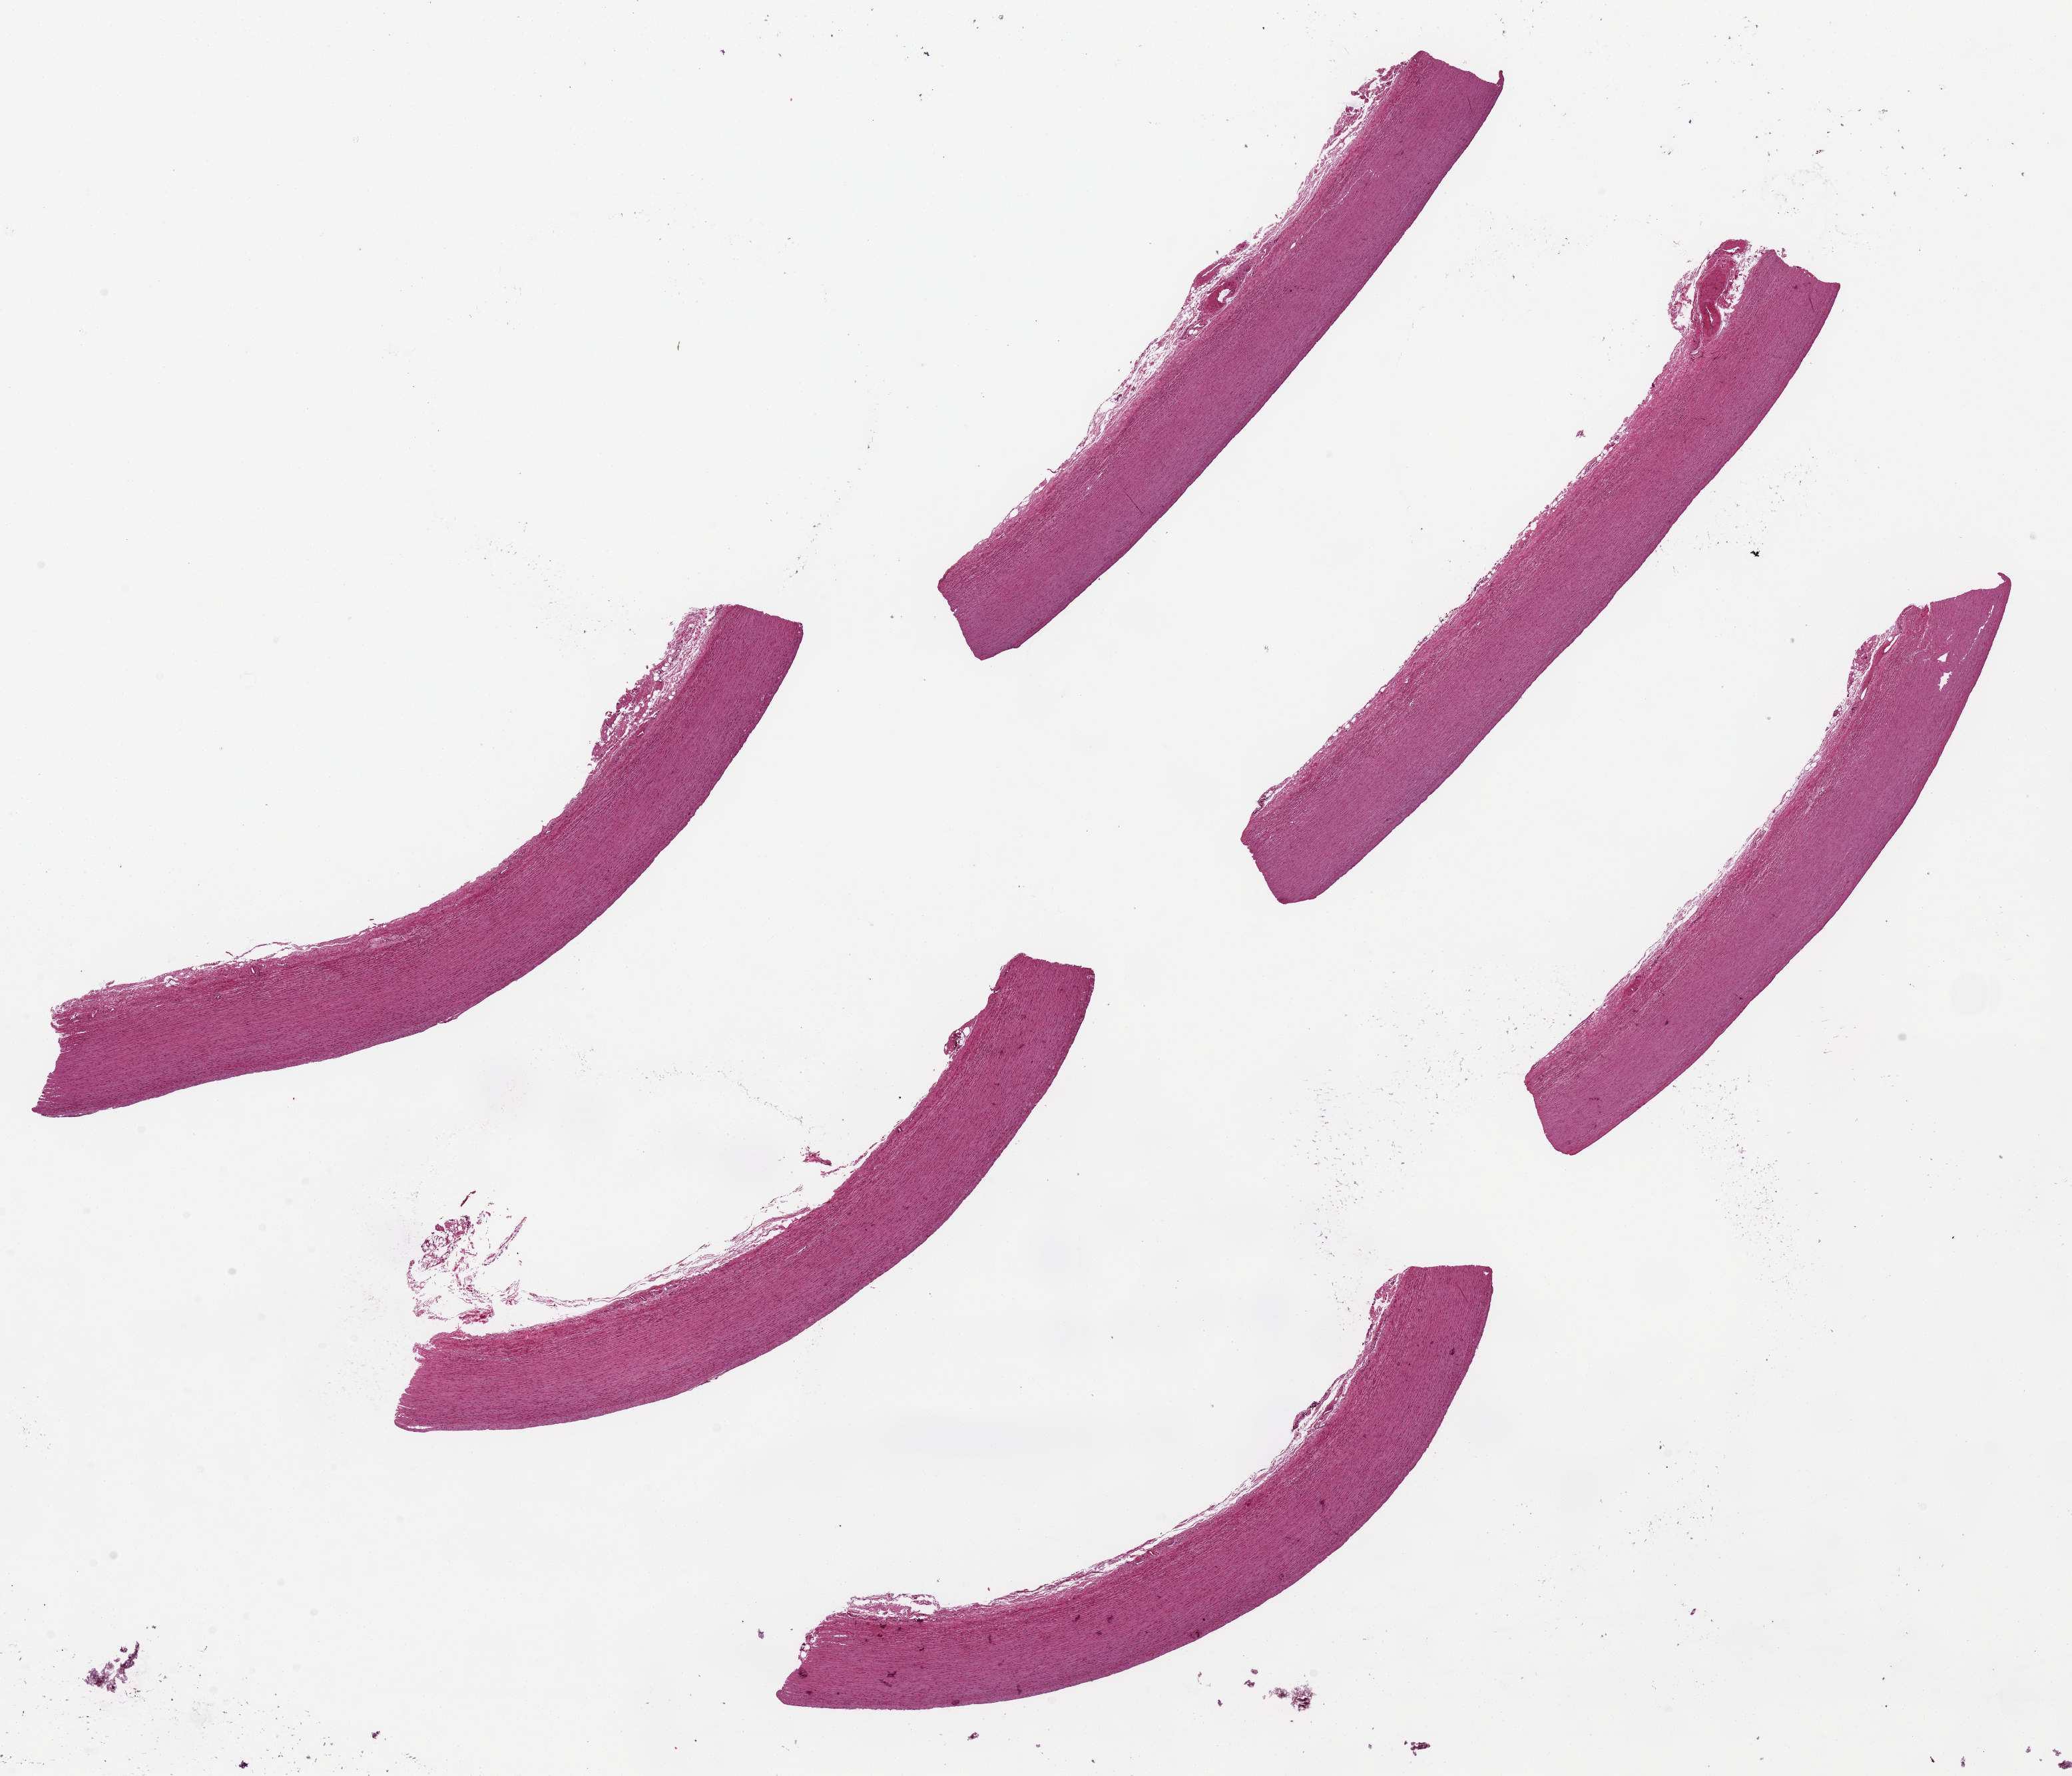
Digitized hematoxylin and eosin (H&E)-stained section, shown as a low-resolution overview of the whole scanned area (about 24.6 x 21.1 mm), PAXgene-fixed, paraffin-embedded tissue, section of aorta (target tissue), tissue donor sample. Donor sex: male.
Reviewer comment on this tissue sample: 6 ~10x1.2mm pieces.